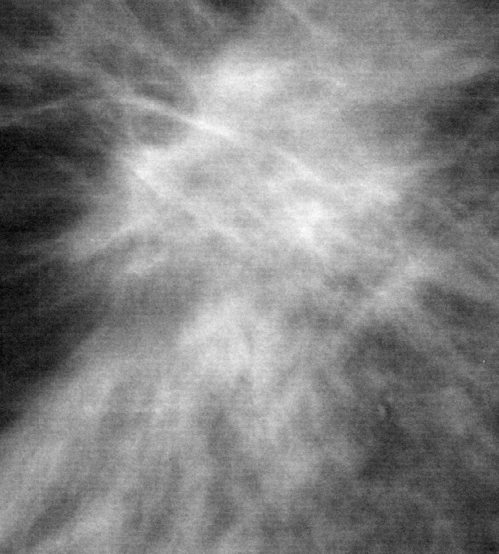
Region of interest cut from a scanned film mammogram (one marked finding); right breast; MLO view; BI-RADS breast density category 2 (scale 1–4).
Mass, shape architectural distortion, margins spiculated; BI-RADS assessment category 2; pathology (as recorded): benign.